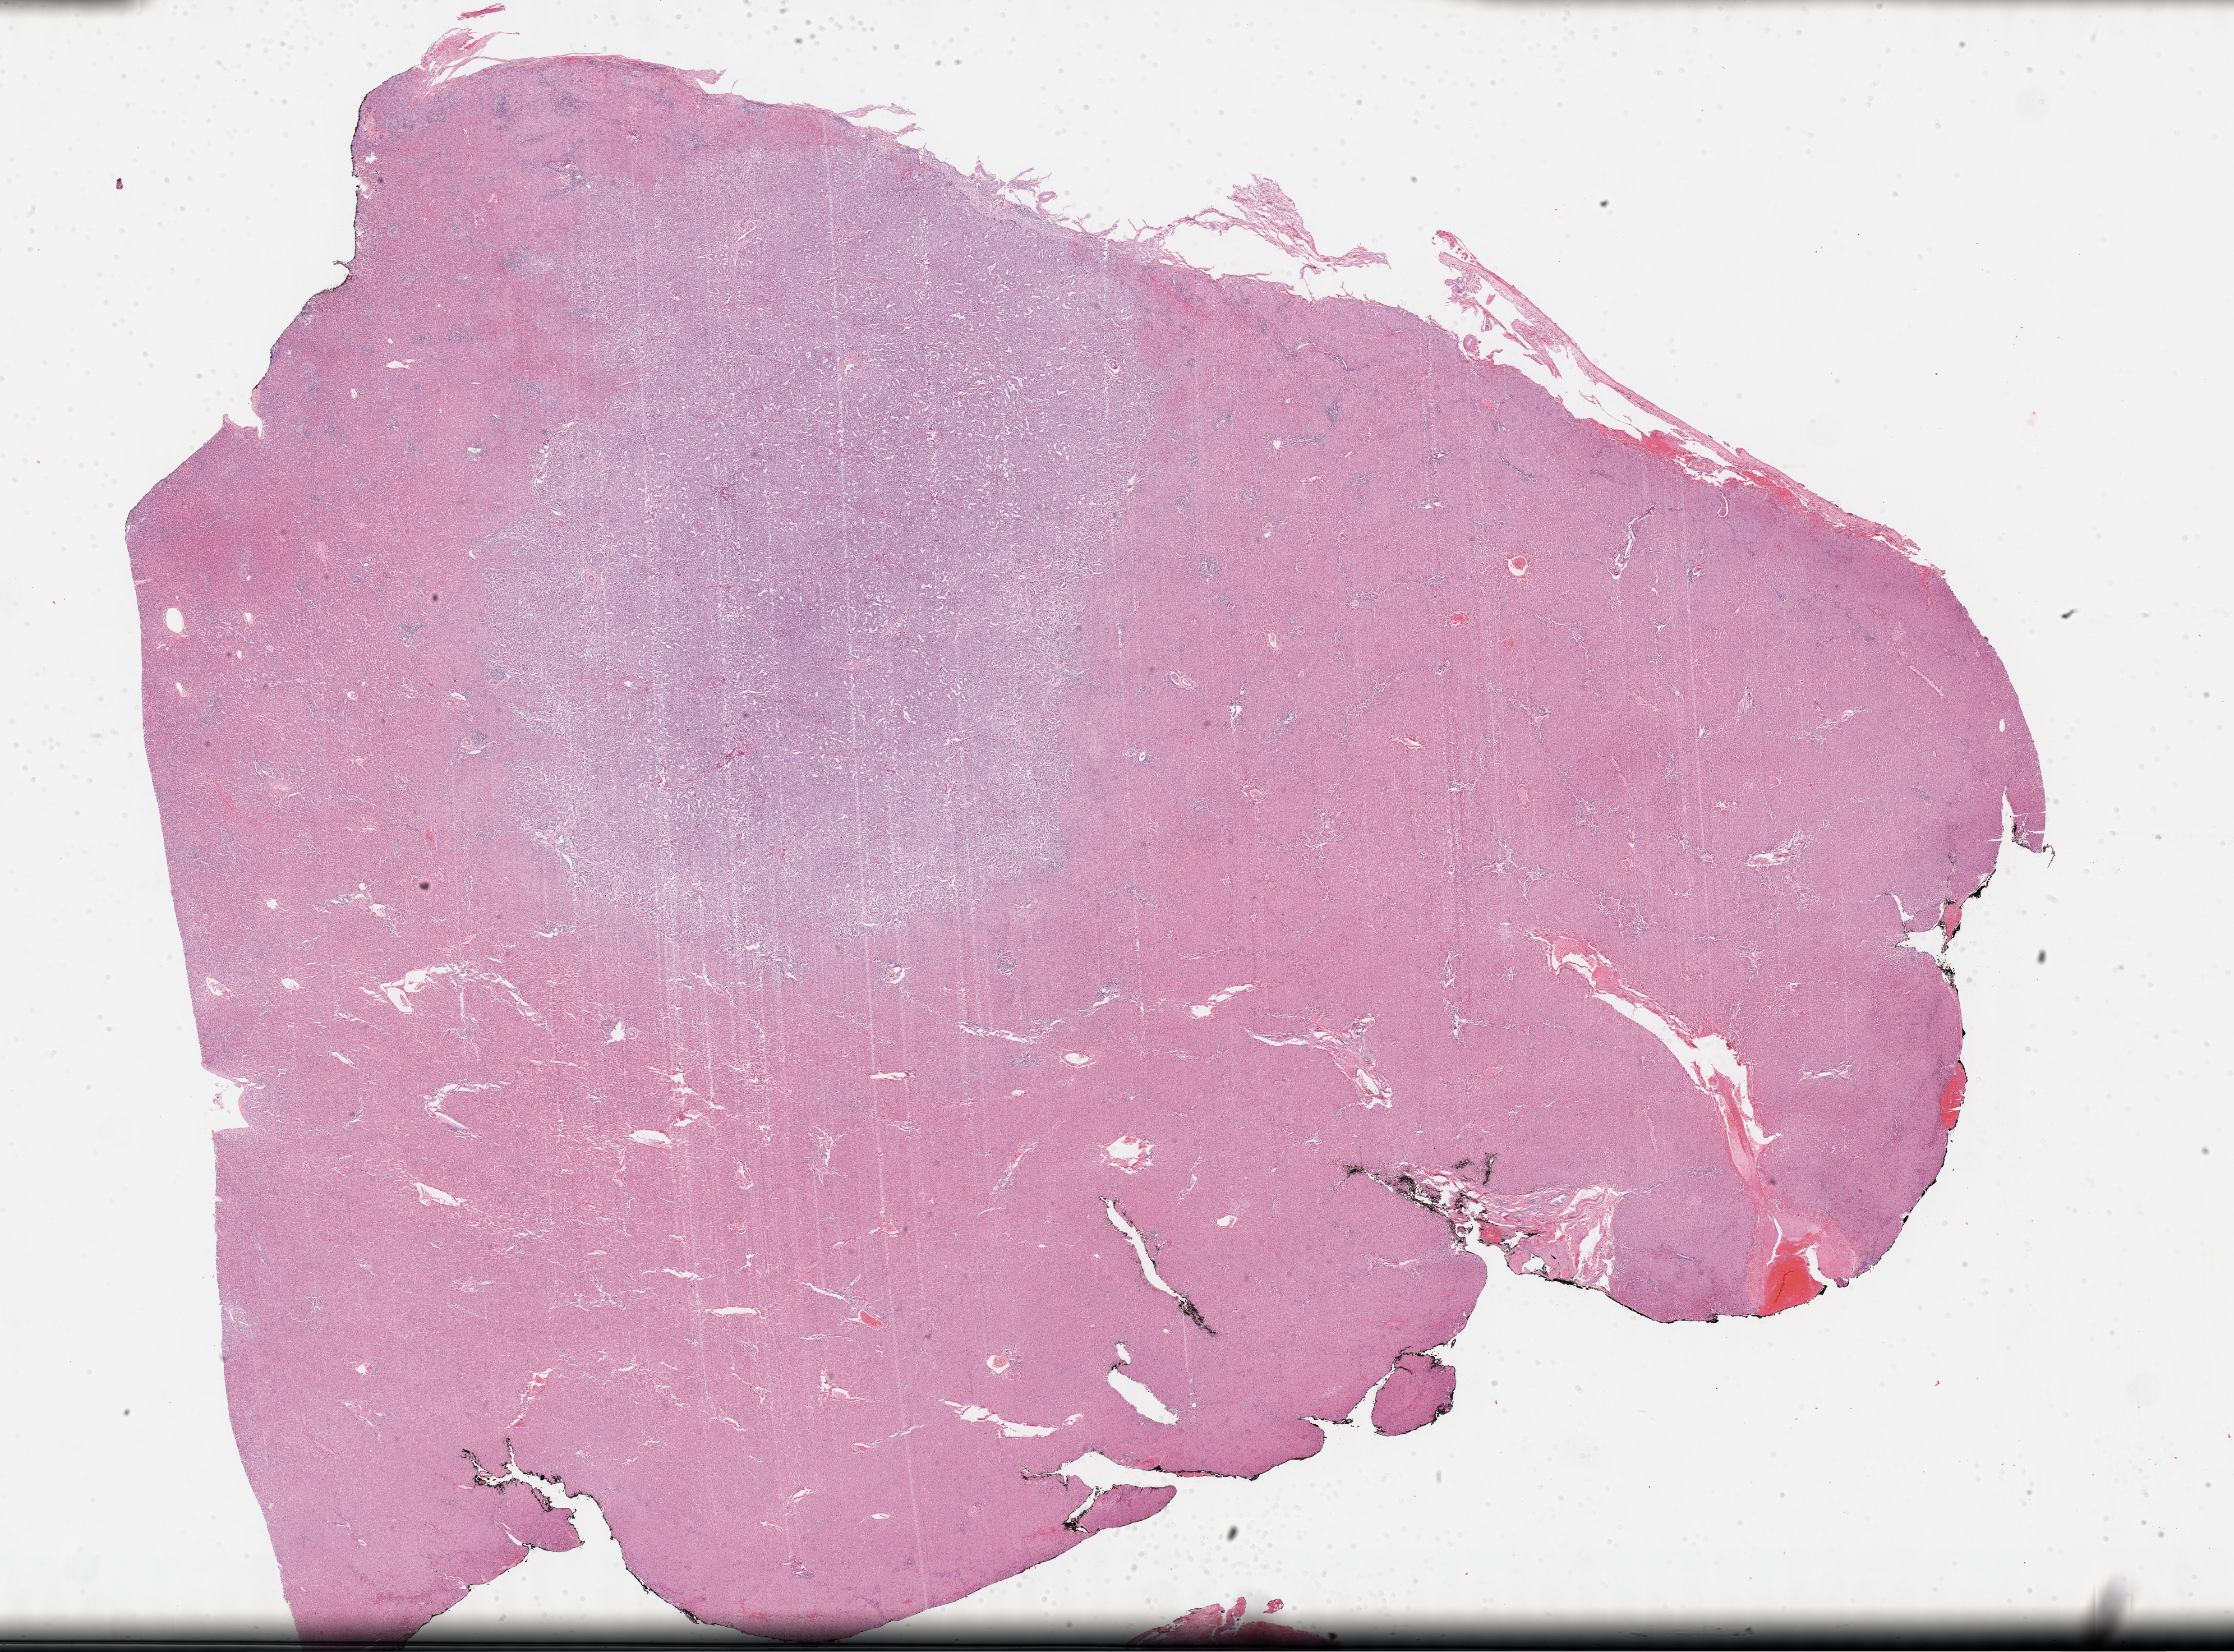
Digitized H&E-stained tissue section (whole slide), low-resolution overview of the scanned area, about 32.2 x 23.8 mm. FFPE section. Primary tumour sample from the bile duct. Patient: female, age at initial diagnosis 62 years. Histologic grade: G2 (moderately differentiated).
Histologic diagnosis: Cholangiocarcinoma. TNM: T3 N0 M0. AJCC pathologic stage: III.